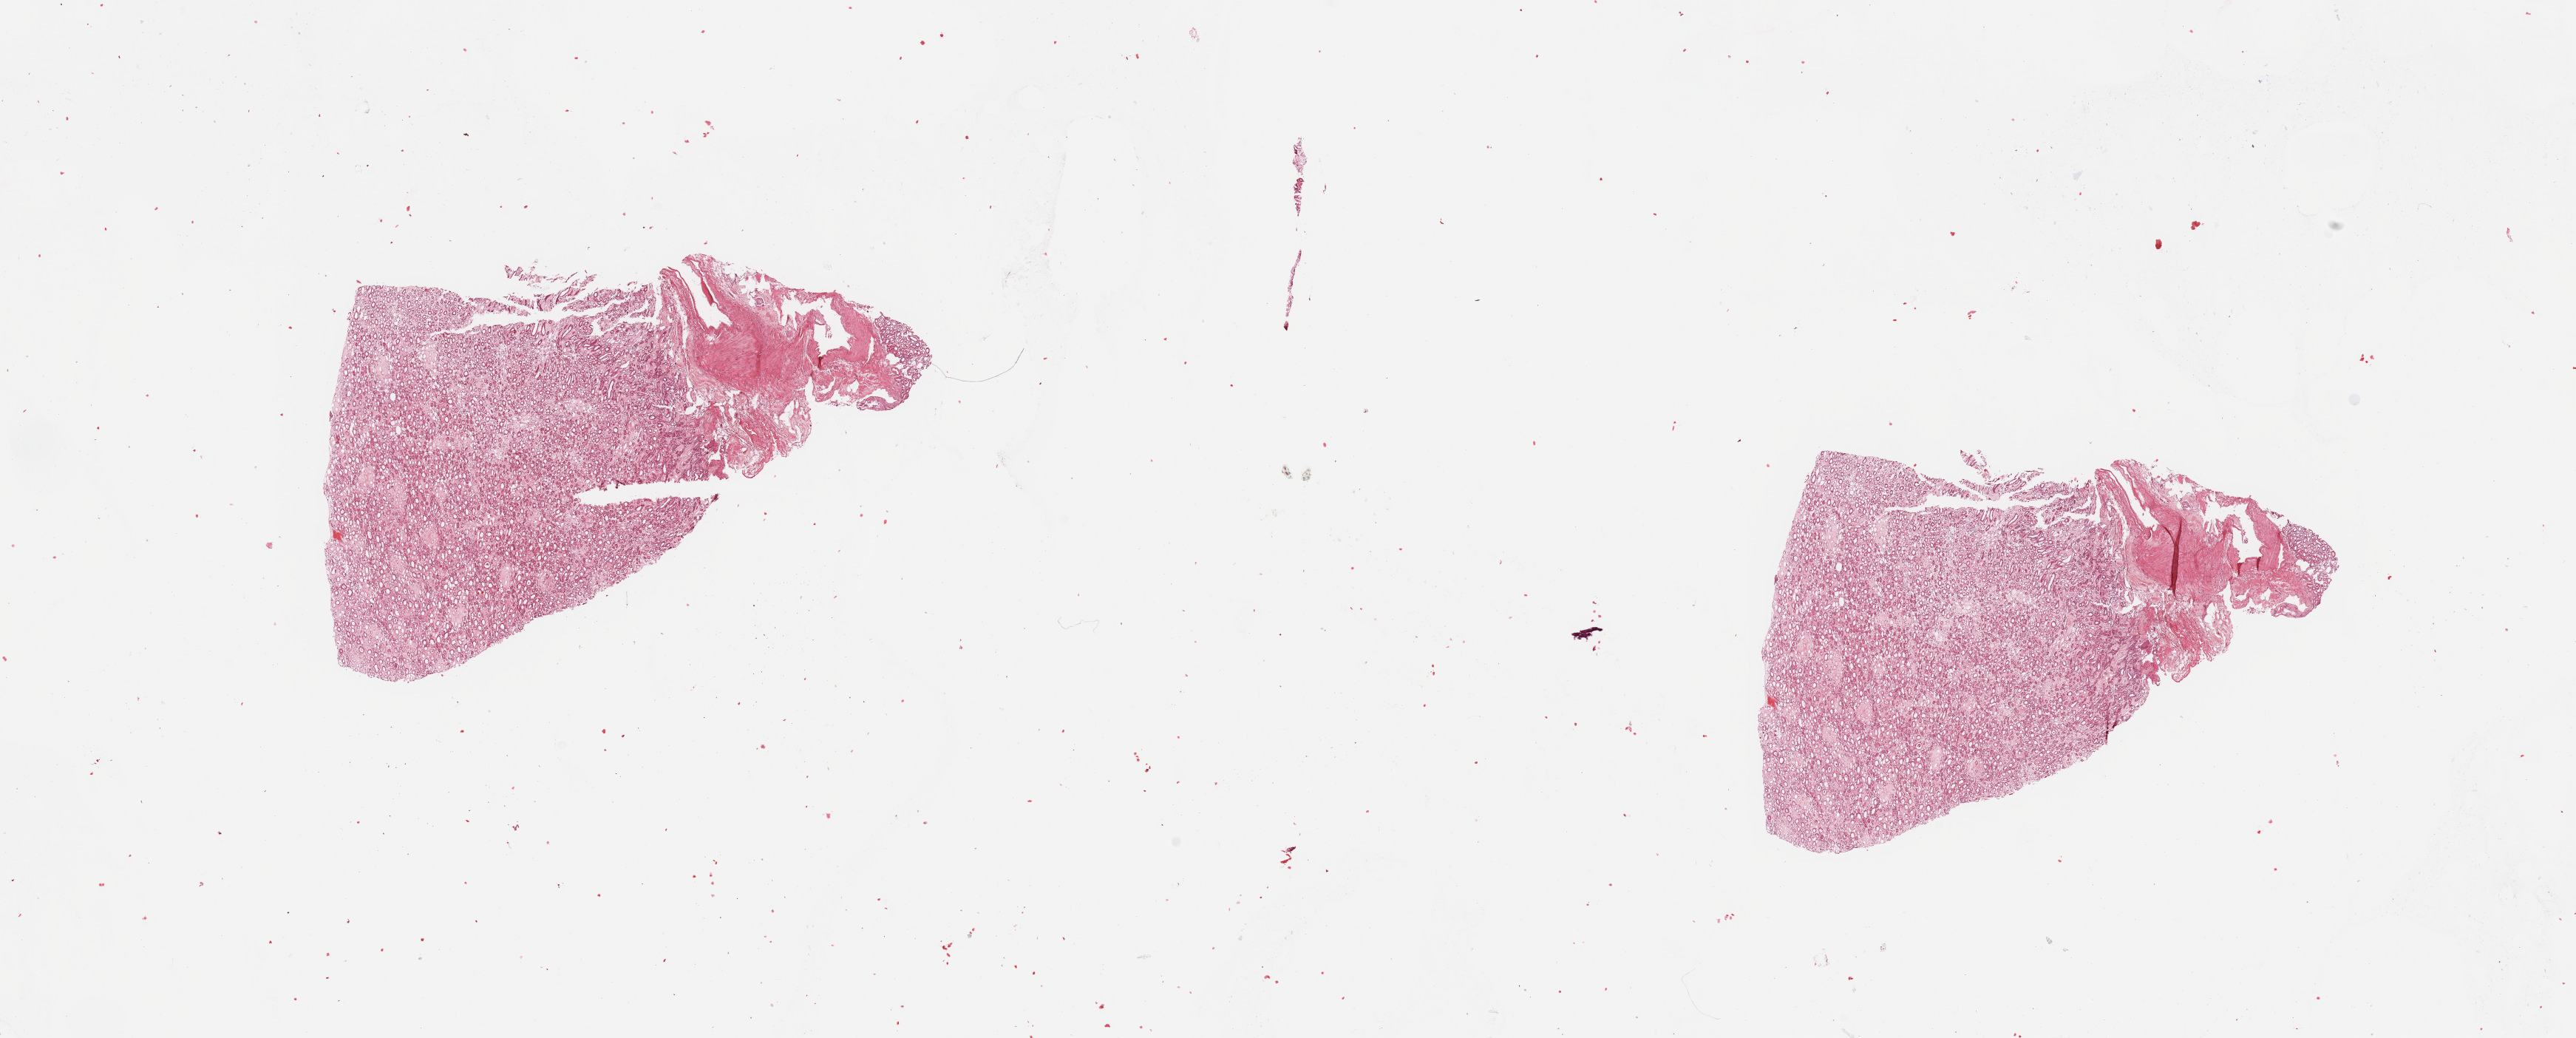
Digitized H&E-stained tissue section (whole slide), a low-resolution overview of the entire scanned area, about 27.6 x 11.1 mm (acquisition: 20x scan), normal (non-tumour) tissue sample, sampled site: kidney. Patient: male, age 71 years.
• this section: normal (non-tumour) tissue from the same patient
• patient diagnosis: Renal cell carcinoma, NOS